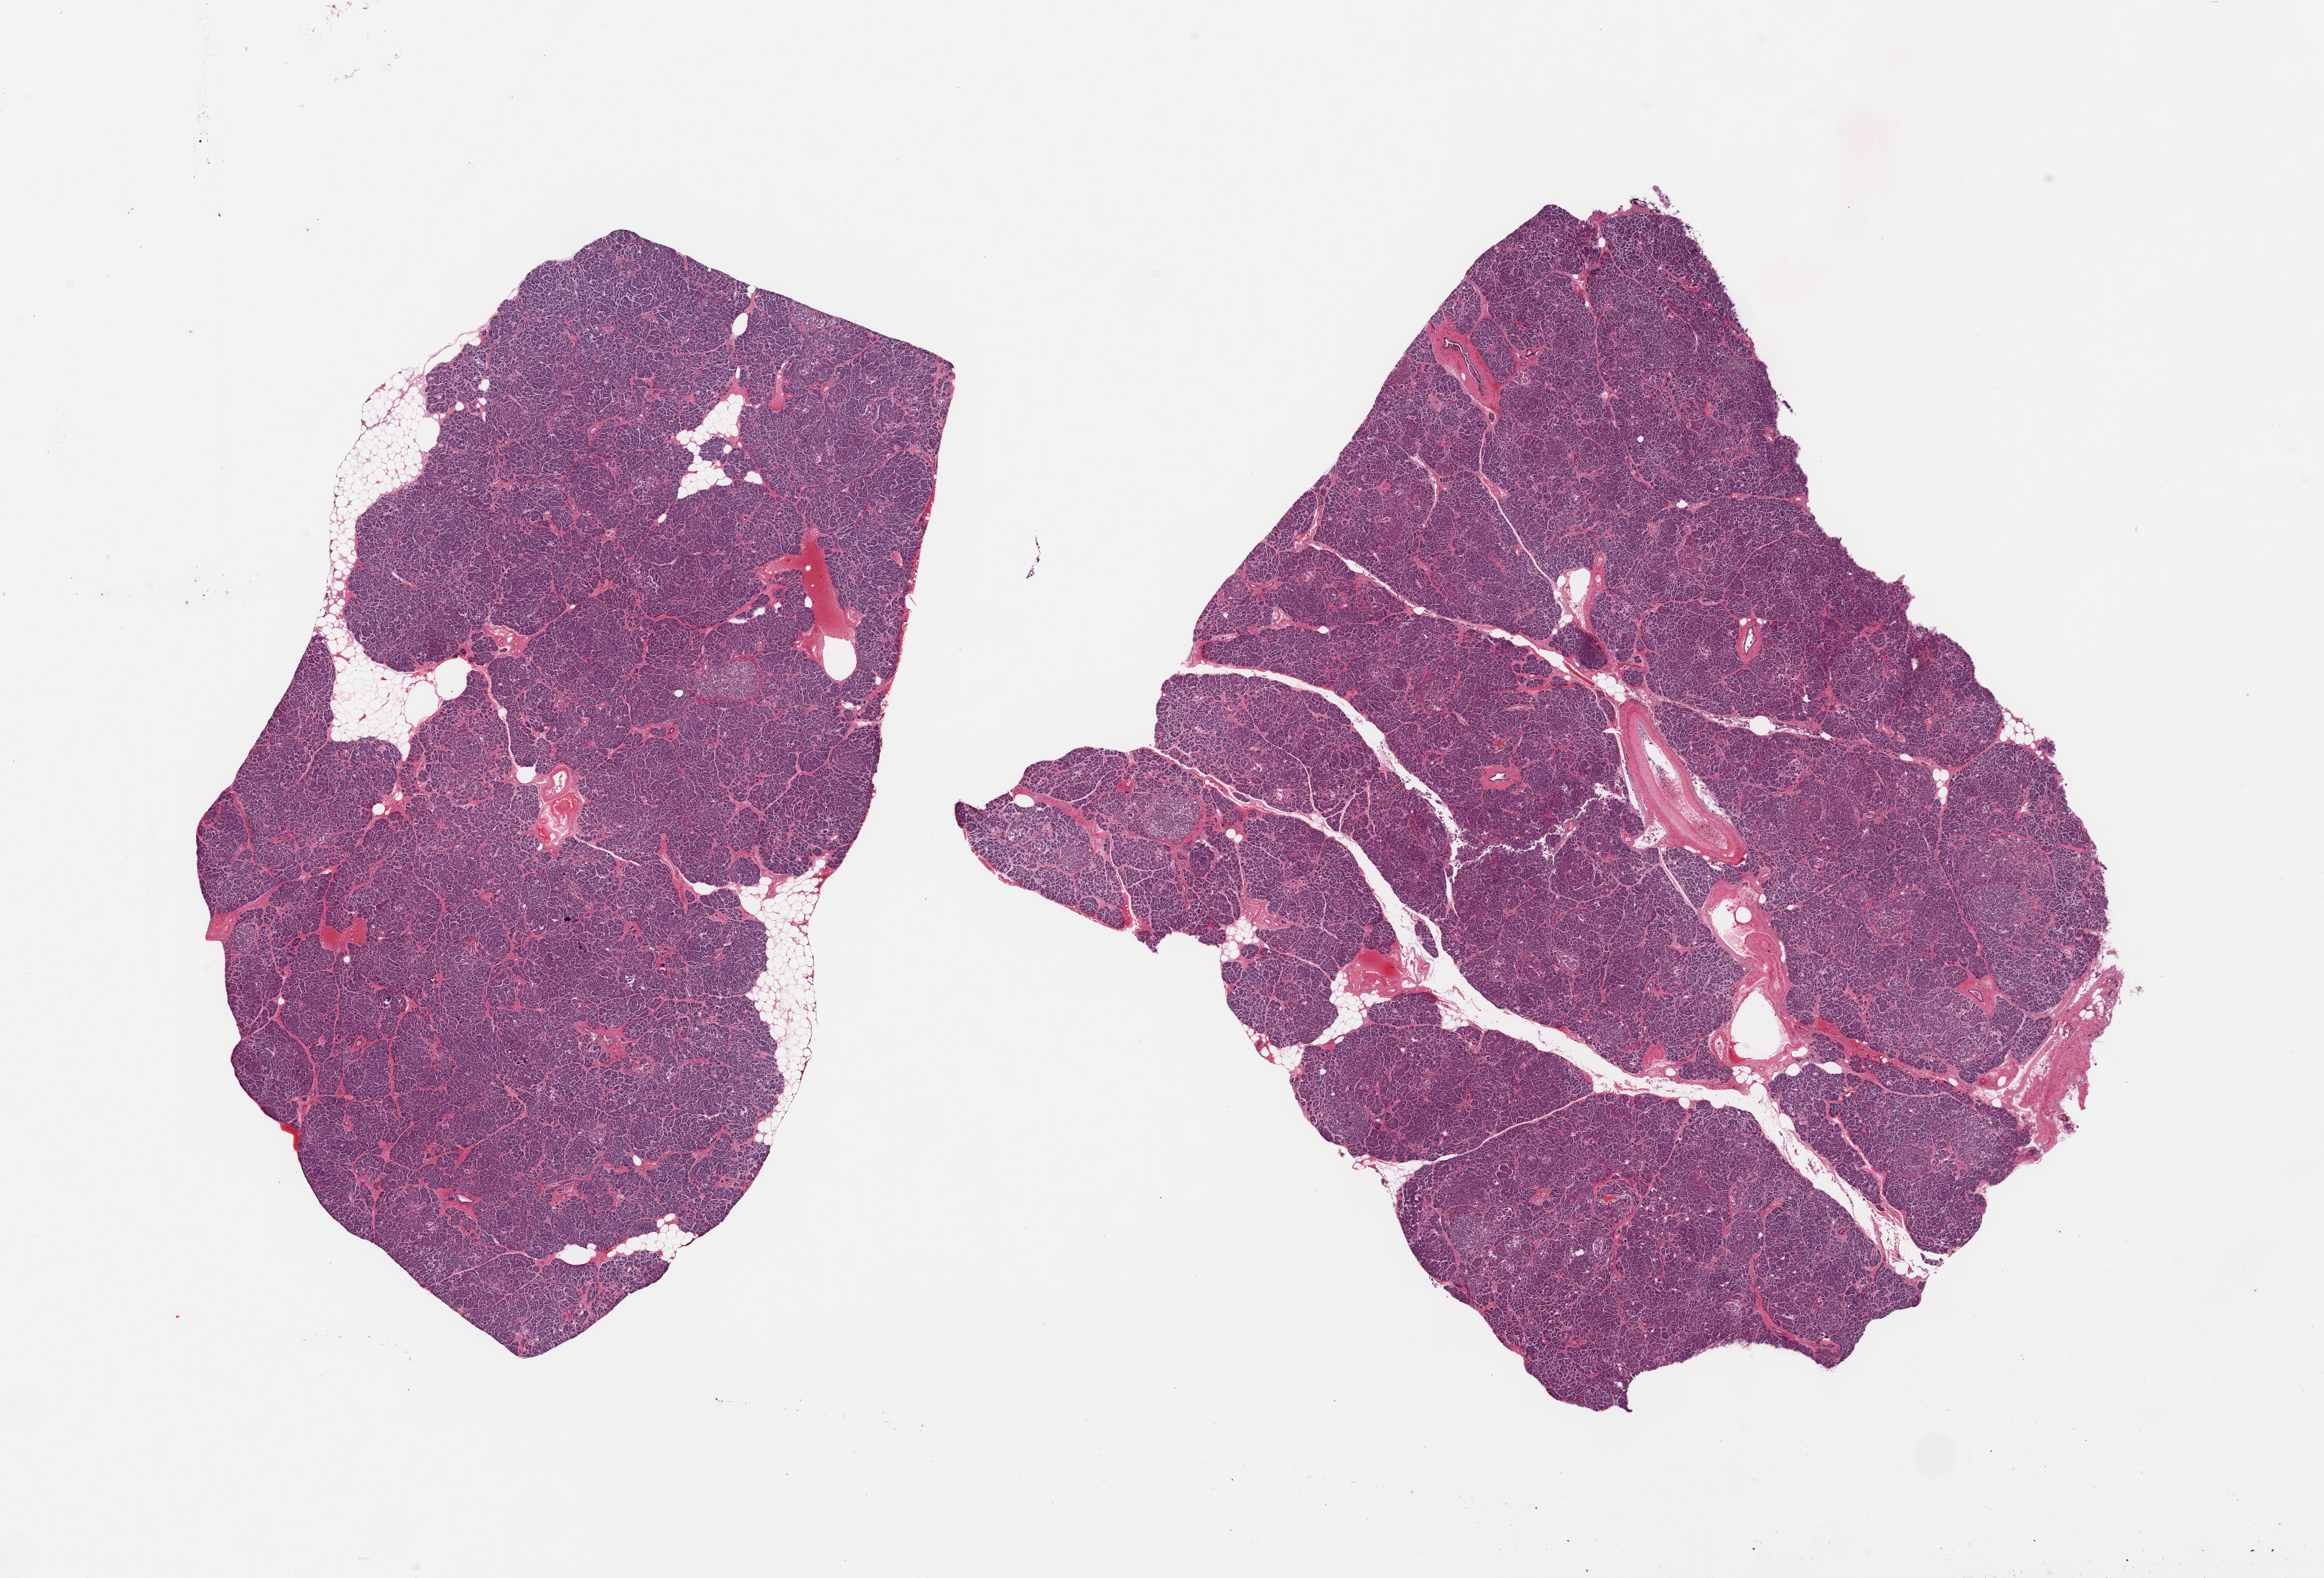
H&E whole-slide image, brightfield, a low-resolution overview of the entire scanned area, about 25.6 x 17.4 mm (from a 20x scan); PAXgene-fixed, paraffin-embedded tissue; sampled site (target tissue): pancreas; donor tissue sample. Male donor.
- reviewer comment on this tissue sample: 2 pieces; <5% external fat